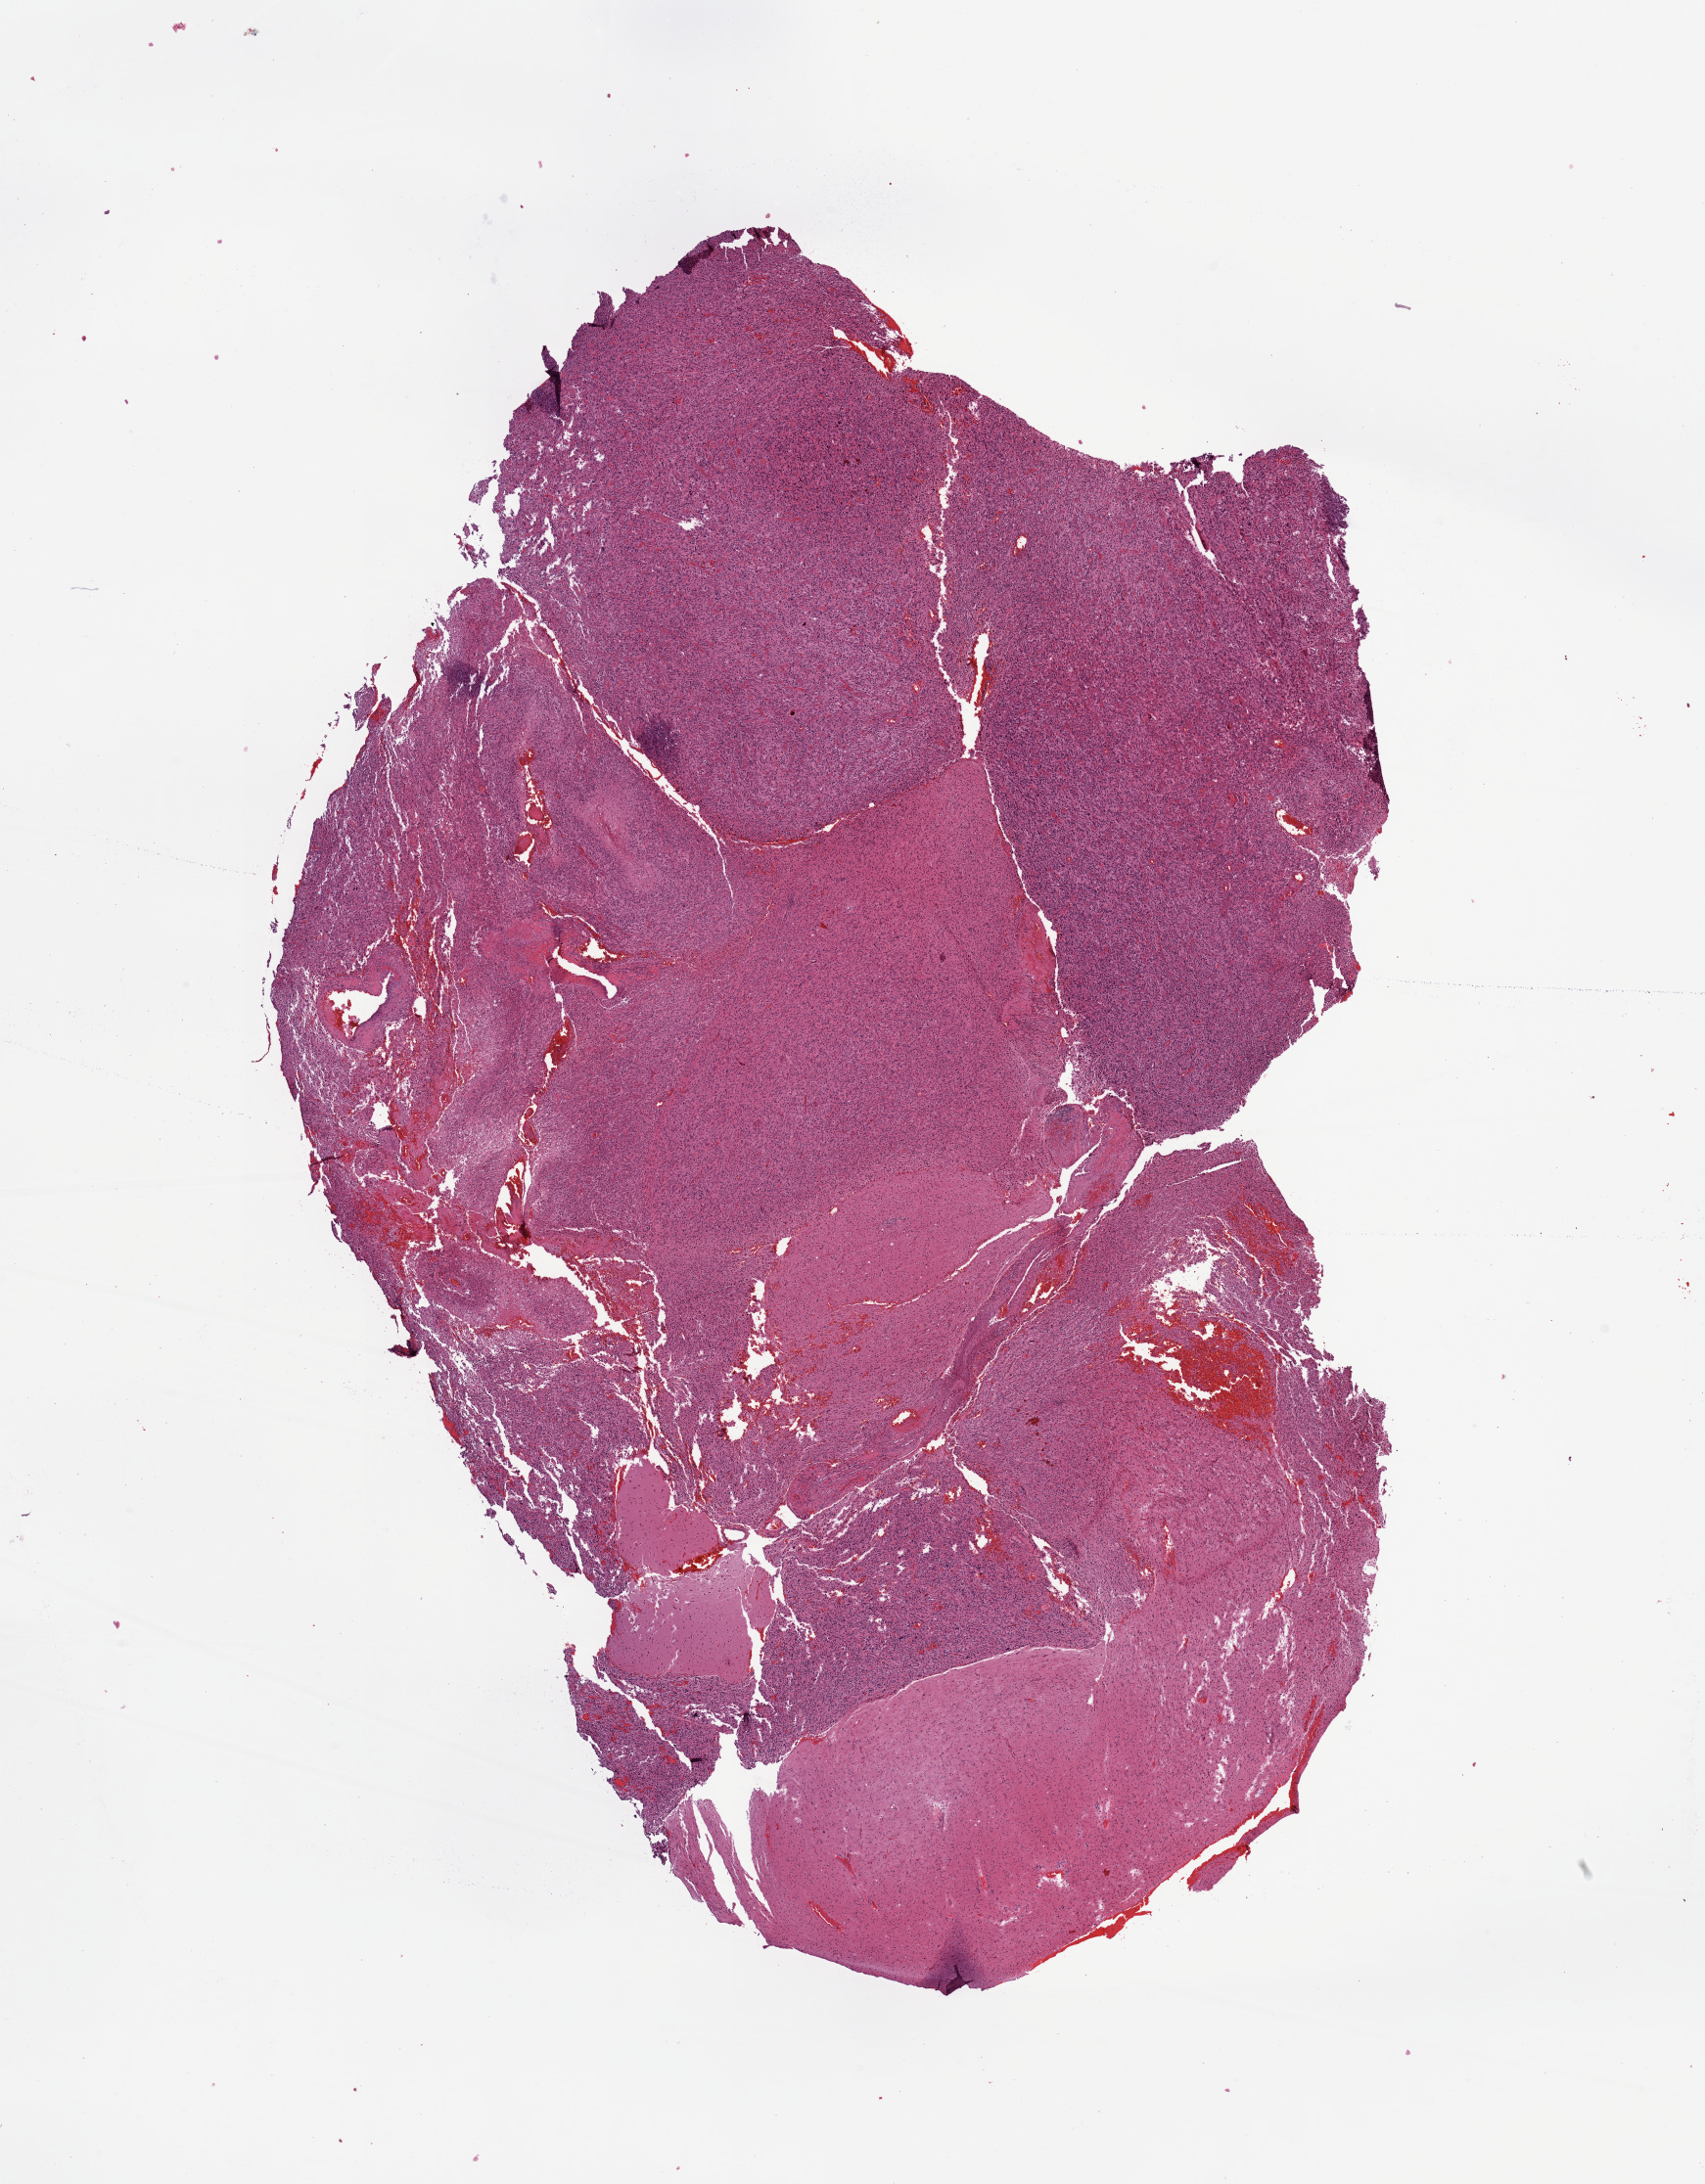
Digitized H&E-stained tissue section (whole slide), low-resolution overview of the scanned area, about 13.8 x 17.7 mm (from a 20x scan); tumour tissue sample, sampled site: brain. Male, 58 y/o. Pathologist review of this section (percent, as recorded): tumour nuclei 80%, necrosis 5%.
• diagnosis: Glioblastoma
• primary tumour site (as recorded): temporal lobe